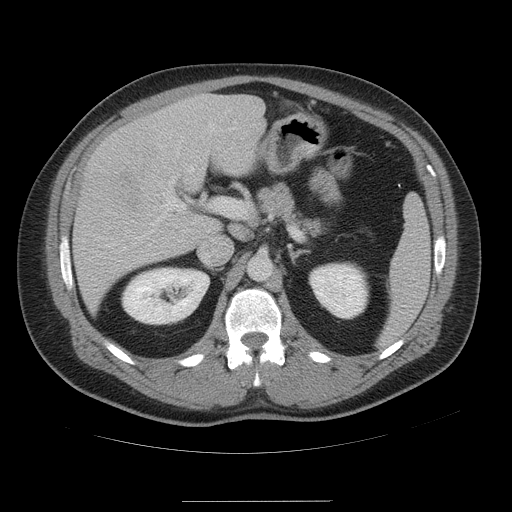
Contrast-enhanced abdominal CT, one axial slice; position 29 of 54 along the scan axis; soft-tissue window (W 400 / L 40 HU); 5 mm slice thickness; 512 × 512 image matrix. Male patient, age 40 years. Case-level facts recorded for this patient, not image findings: diagnosis: colorectal cancer liver metastases, imaged before liver resection; multiple liver metastases: no; largest metastasis: 15 cm.
Outlined on this slice (outlined manually by an expert reader):
- hepatic veins: bounding box (x1, y1, x2, y2) in pixels: (188, 129, 215, 172)
- liver: (73, 95, 266, 315)
- planned liver remnant (the part of the liver to remain after resection): (208, 95, 266, 176)
- portal vein (with intrahepatic branches): (151, 193, 244, 225)
- liver metastasis: (120, 155, 150, 207)